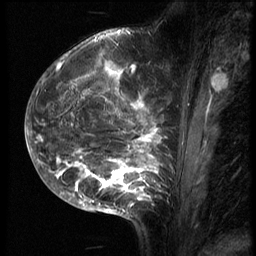
Breast MRI (dynamic contrast-enhanced), one sagittal slice. Position 26 of 70 along the scan axis. 3 images stored at this slice position (order not interpretable as contrast timing). 1.5 T. TE 4.2 ms, TR 9 ms. 2.5 mm slice thickness. 256 × 256 image matrix, field of view 180 × 180 mm. Patient: female, 28 years. From the clinical record (not read from this slice): setting: breast cancer imaged before/during neoadjuvant chemotherapy.
Structures marked on this image (semi-automatic segmentation, software-assisted and operator-edited):
- analysis volume of interest (the breast-tissue region the enhancement analysis was run in; not a lesion): bounding box [x1, y1, x2, y2] px = [43, 42, 186, 215]
- tumour enhancement mask (voxels above the 140 % enhancement threshold inside the analysis volume of interest): [43, 50, 168, 213]